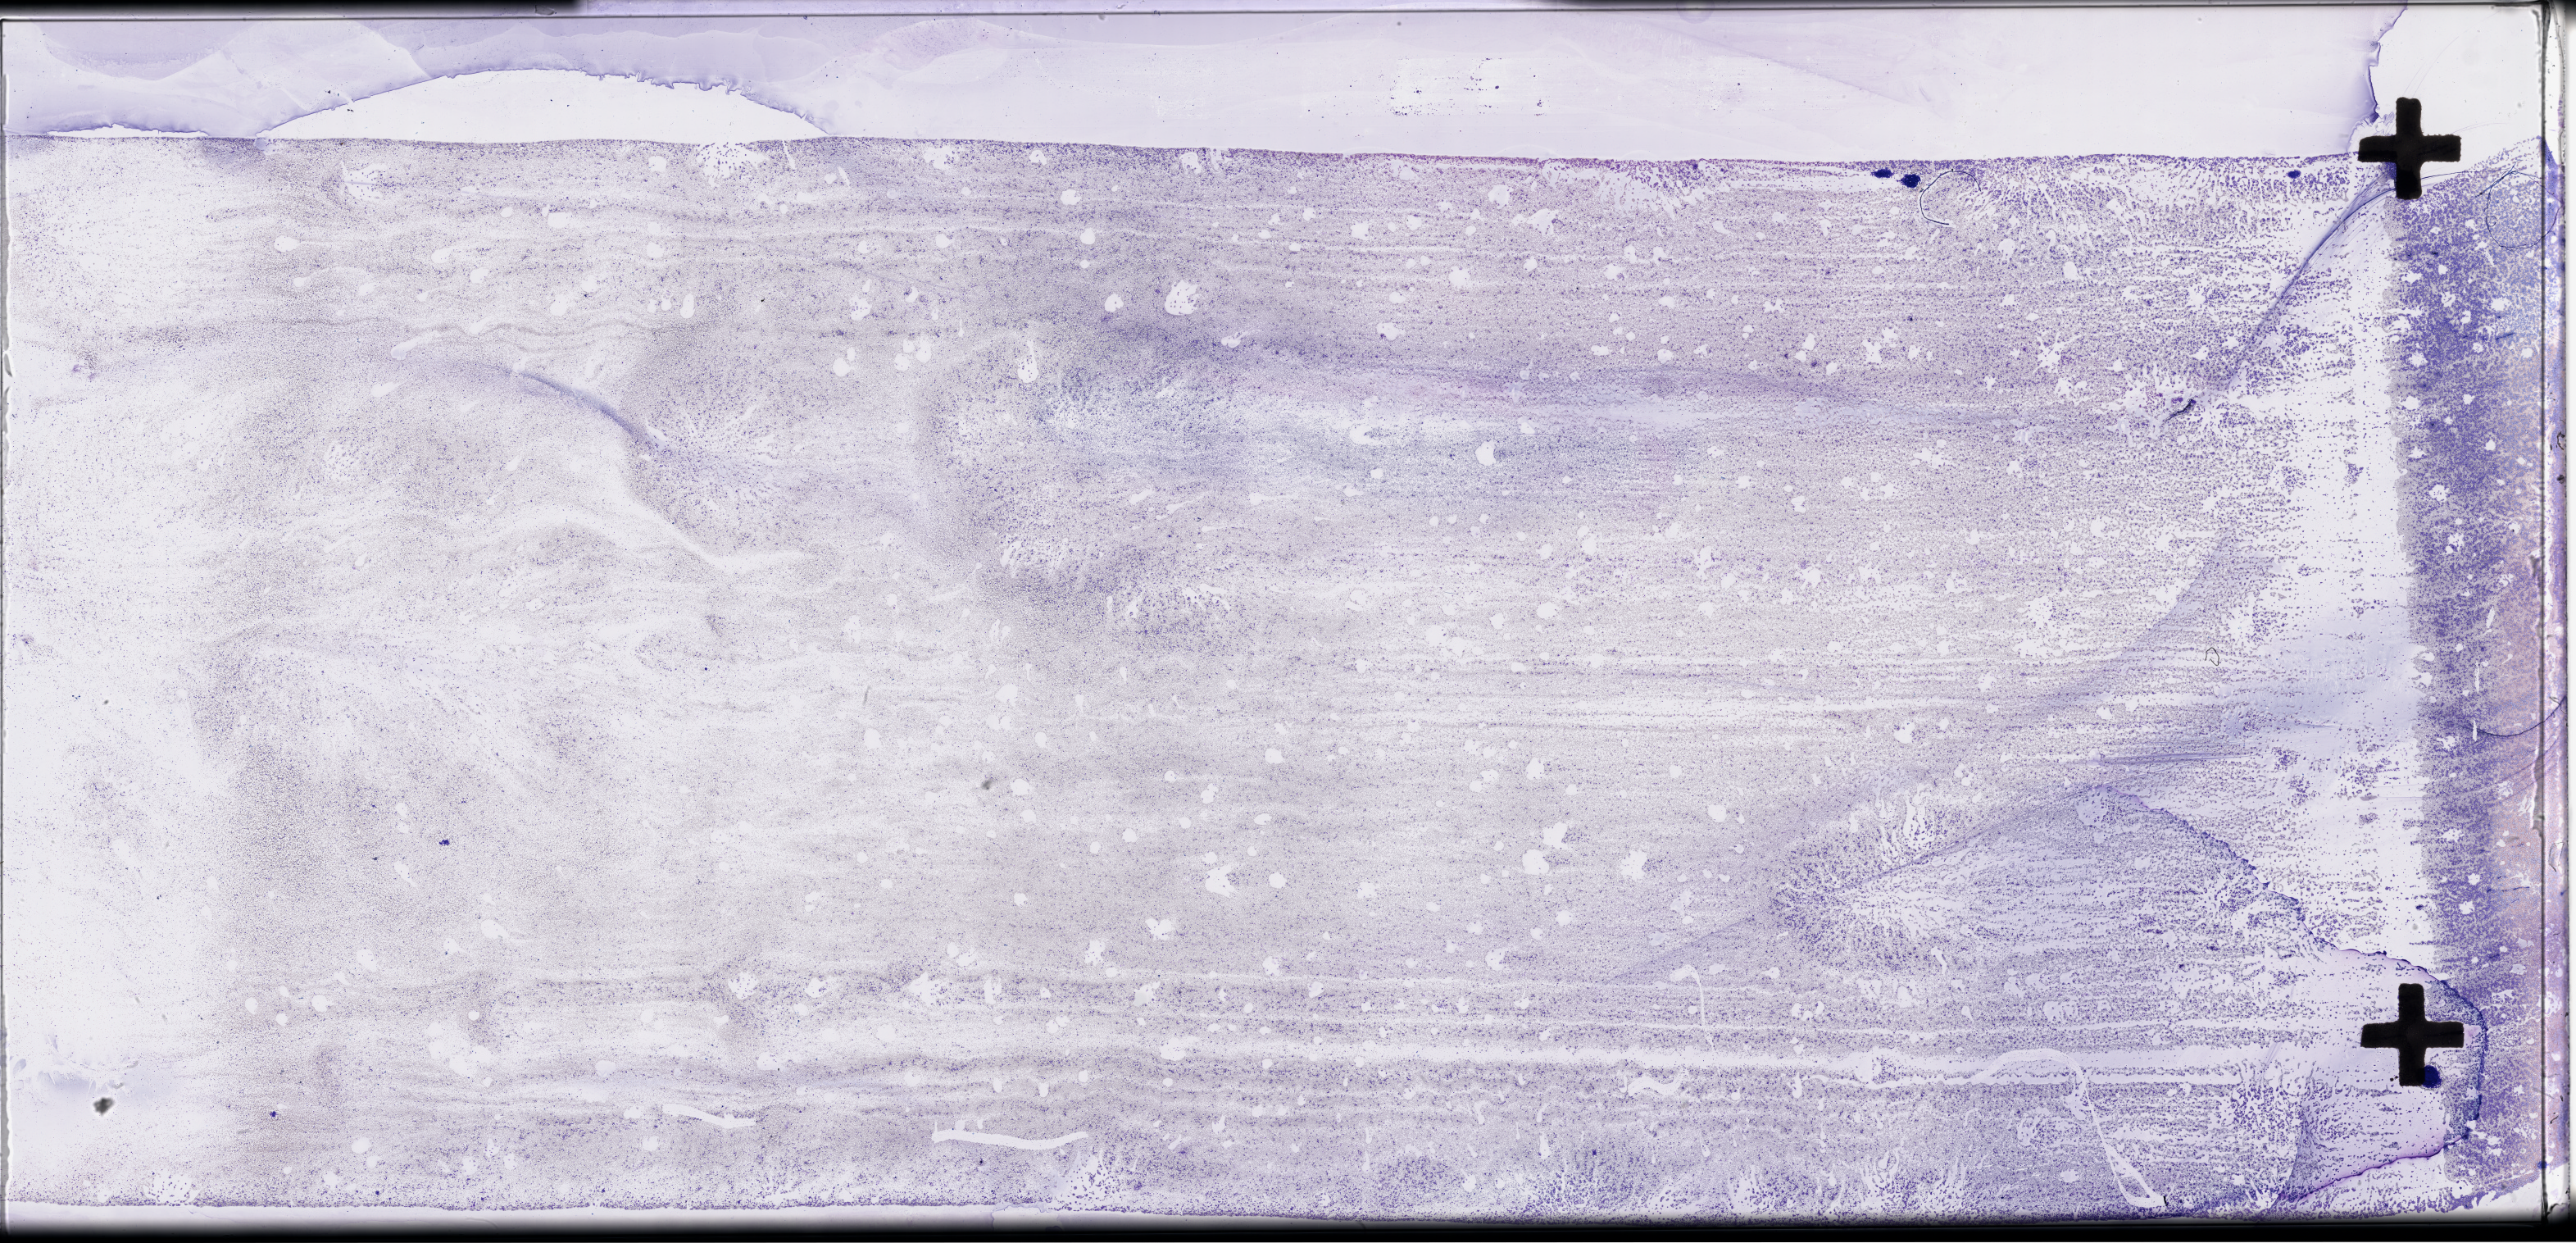
H&E-stained whole-slide image, shown as a low-resolution overview of the whole scanned area (about 50.8 x 24.5 mm); bone marrow (leukaemic) sample. Patient: female, age 58 years. Blasts: 60%.
WHO classification: Acute monoblastic and monocytic leukemia. FAB classification: M5. Diagnosis: Acute Myeloid Leukemia.